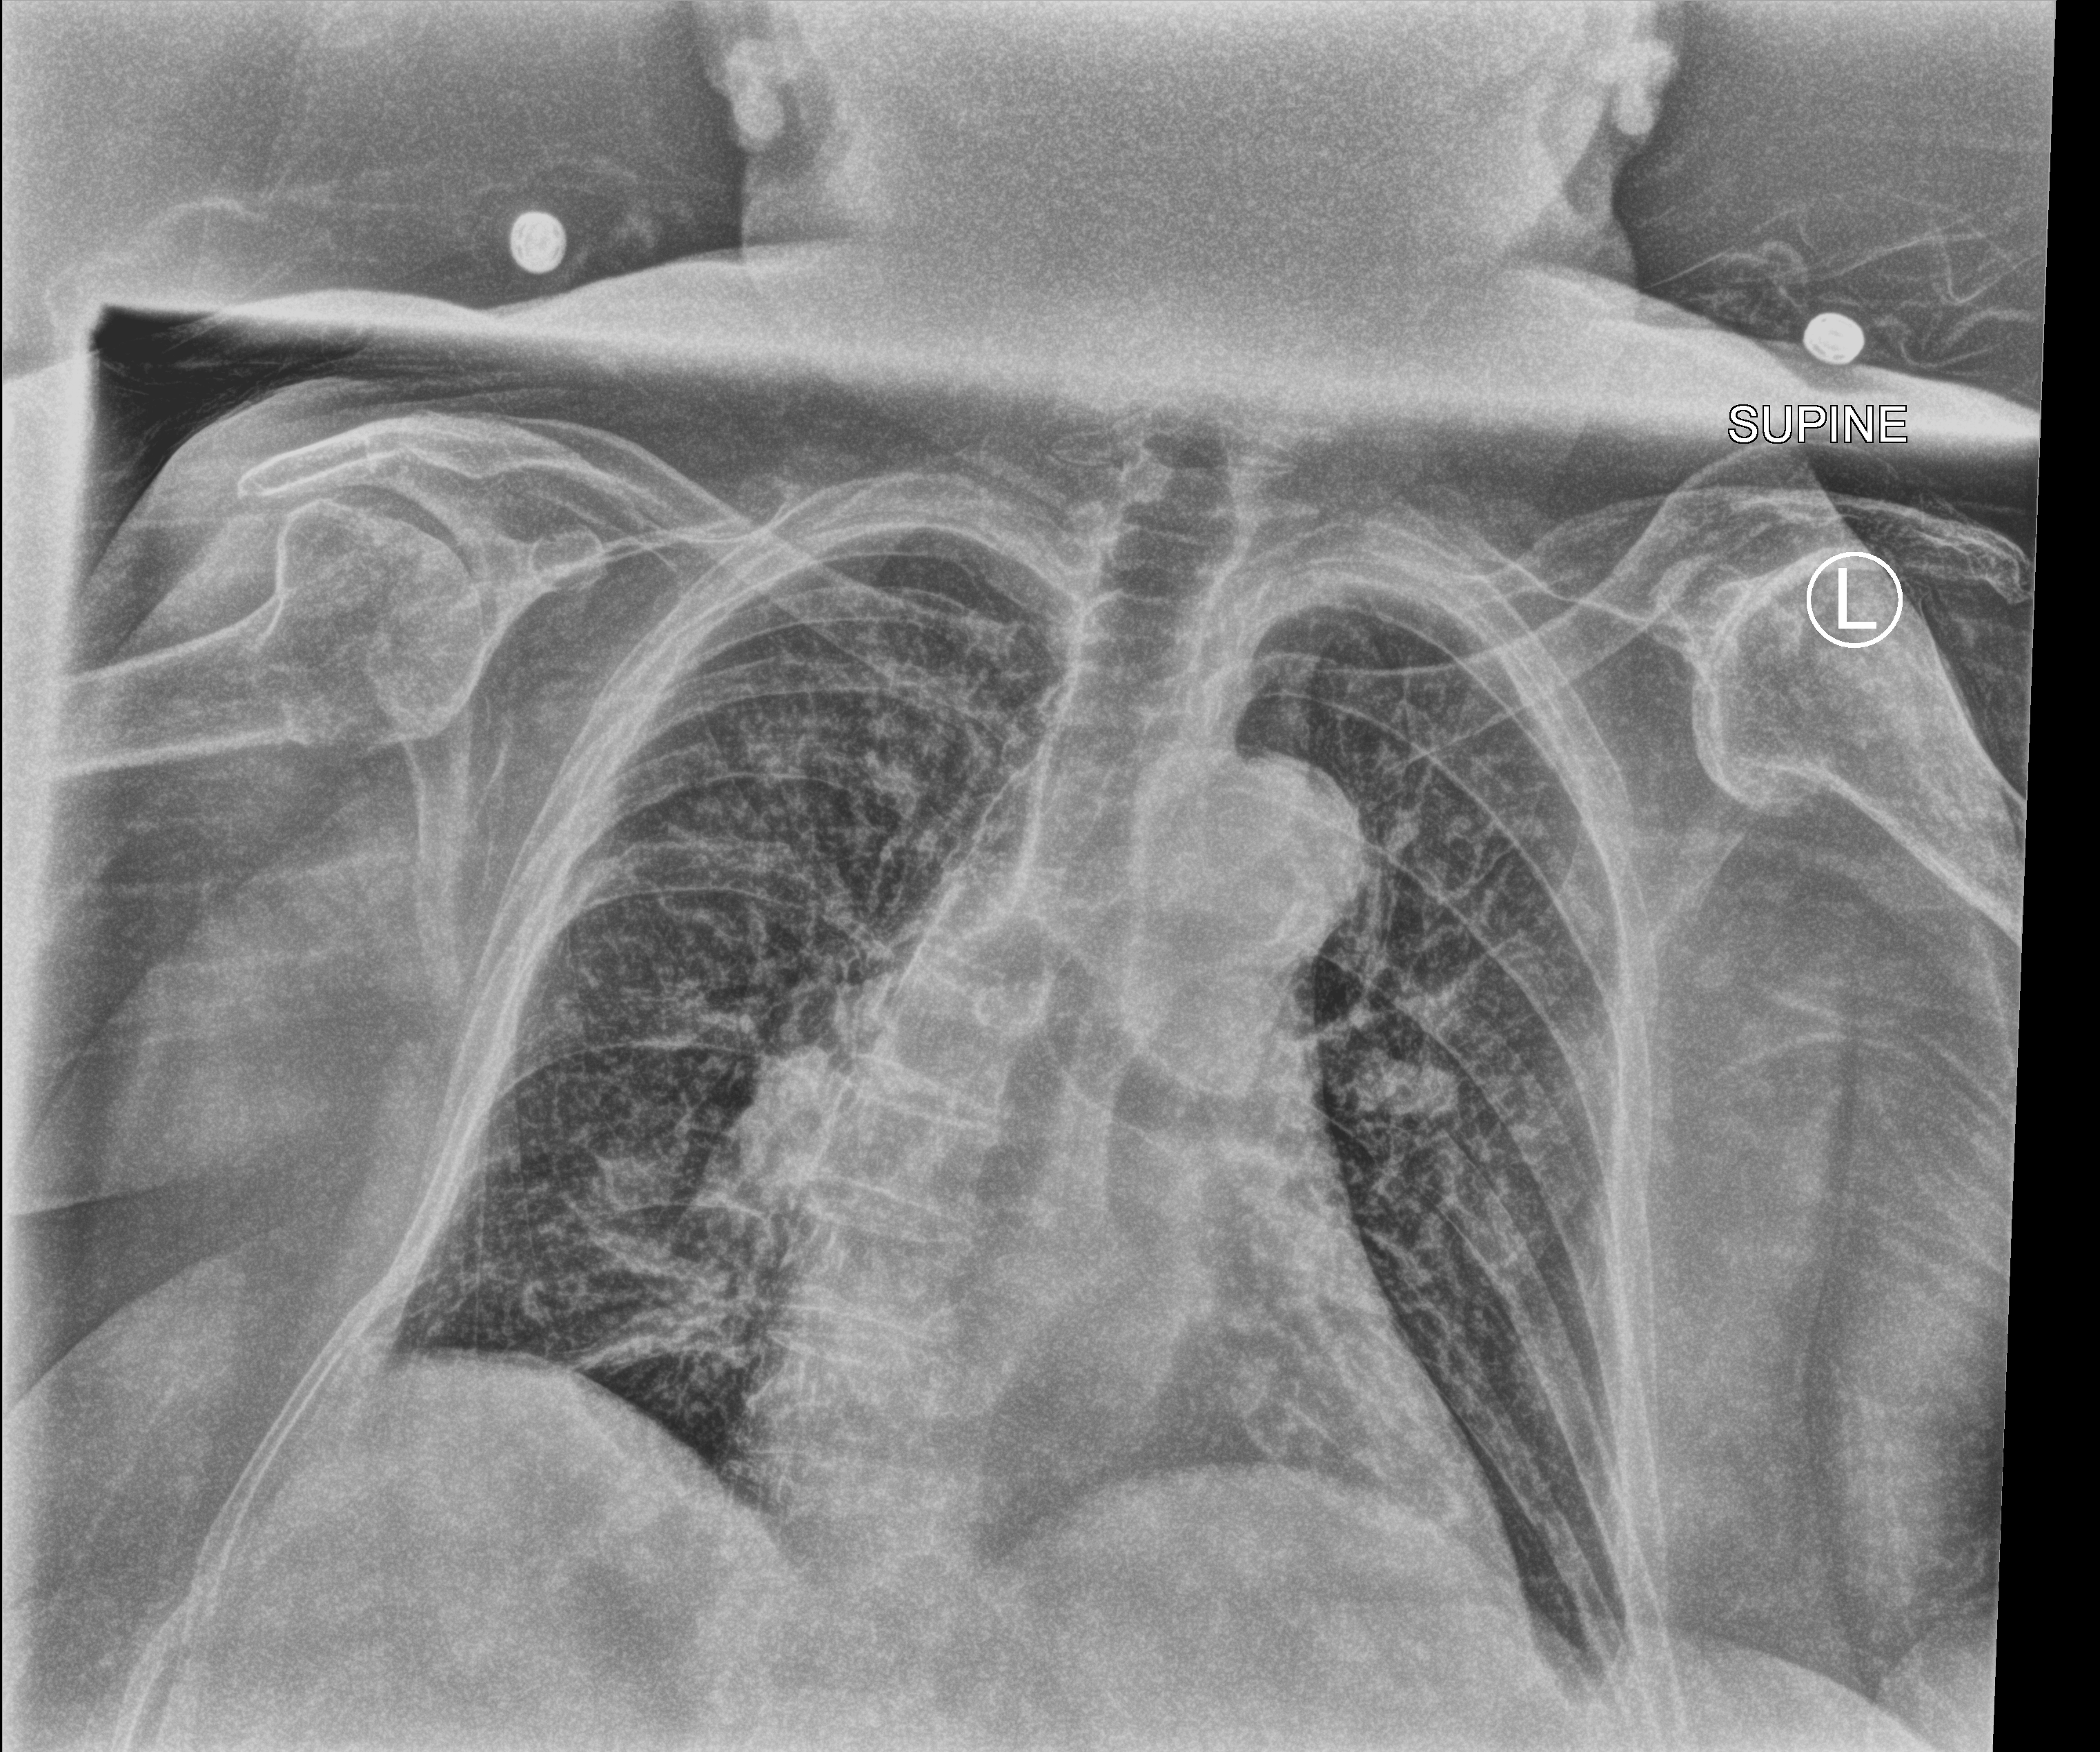
Portable chest radiograph, anteroposterior (AP) projection. Female patient hospitalised with COVID-19, age 75–90 years.
From the hospital-stay record, not from the radiograph (when in the stay this image was taken is not recorded): admitted to intensive care during this hospital stay: yes; mechanically ventilated during this hospital stay: no.